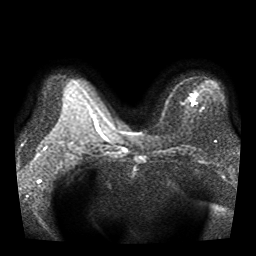
Breast MRI, one axial slice; slice 22 of 40 in the series (ordered by position); diffusion-weighted series; image 2 of 4 stored at this slice position (different b-values; order by instance number); 1.5 T; 256 × 256 image matrix, field of view 330 × 330 mm. Female patient.
Annotated regions visible in this slice (manually delineated by an expert):
- tumour on diffusion-weighted imaging: bounding box <189,94,198,107> (left, top, right, bottom; pixels)